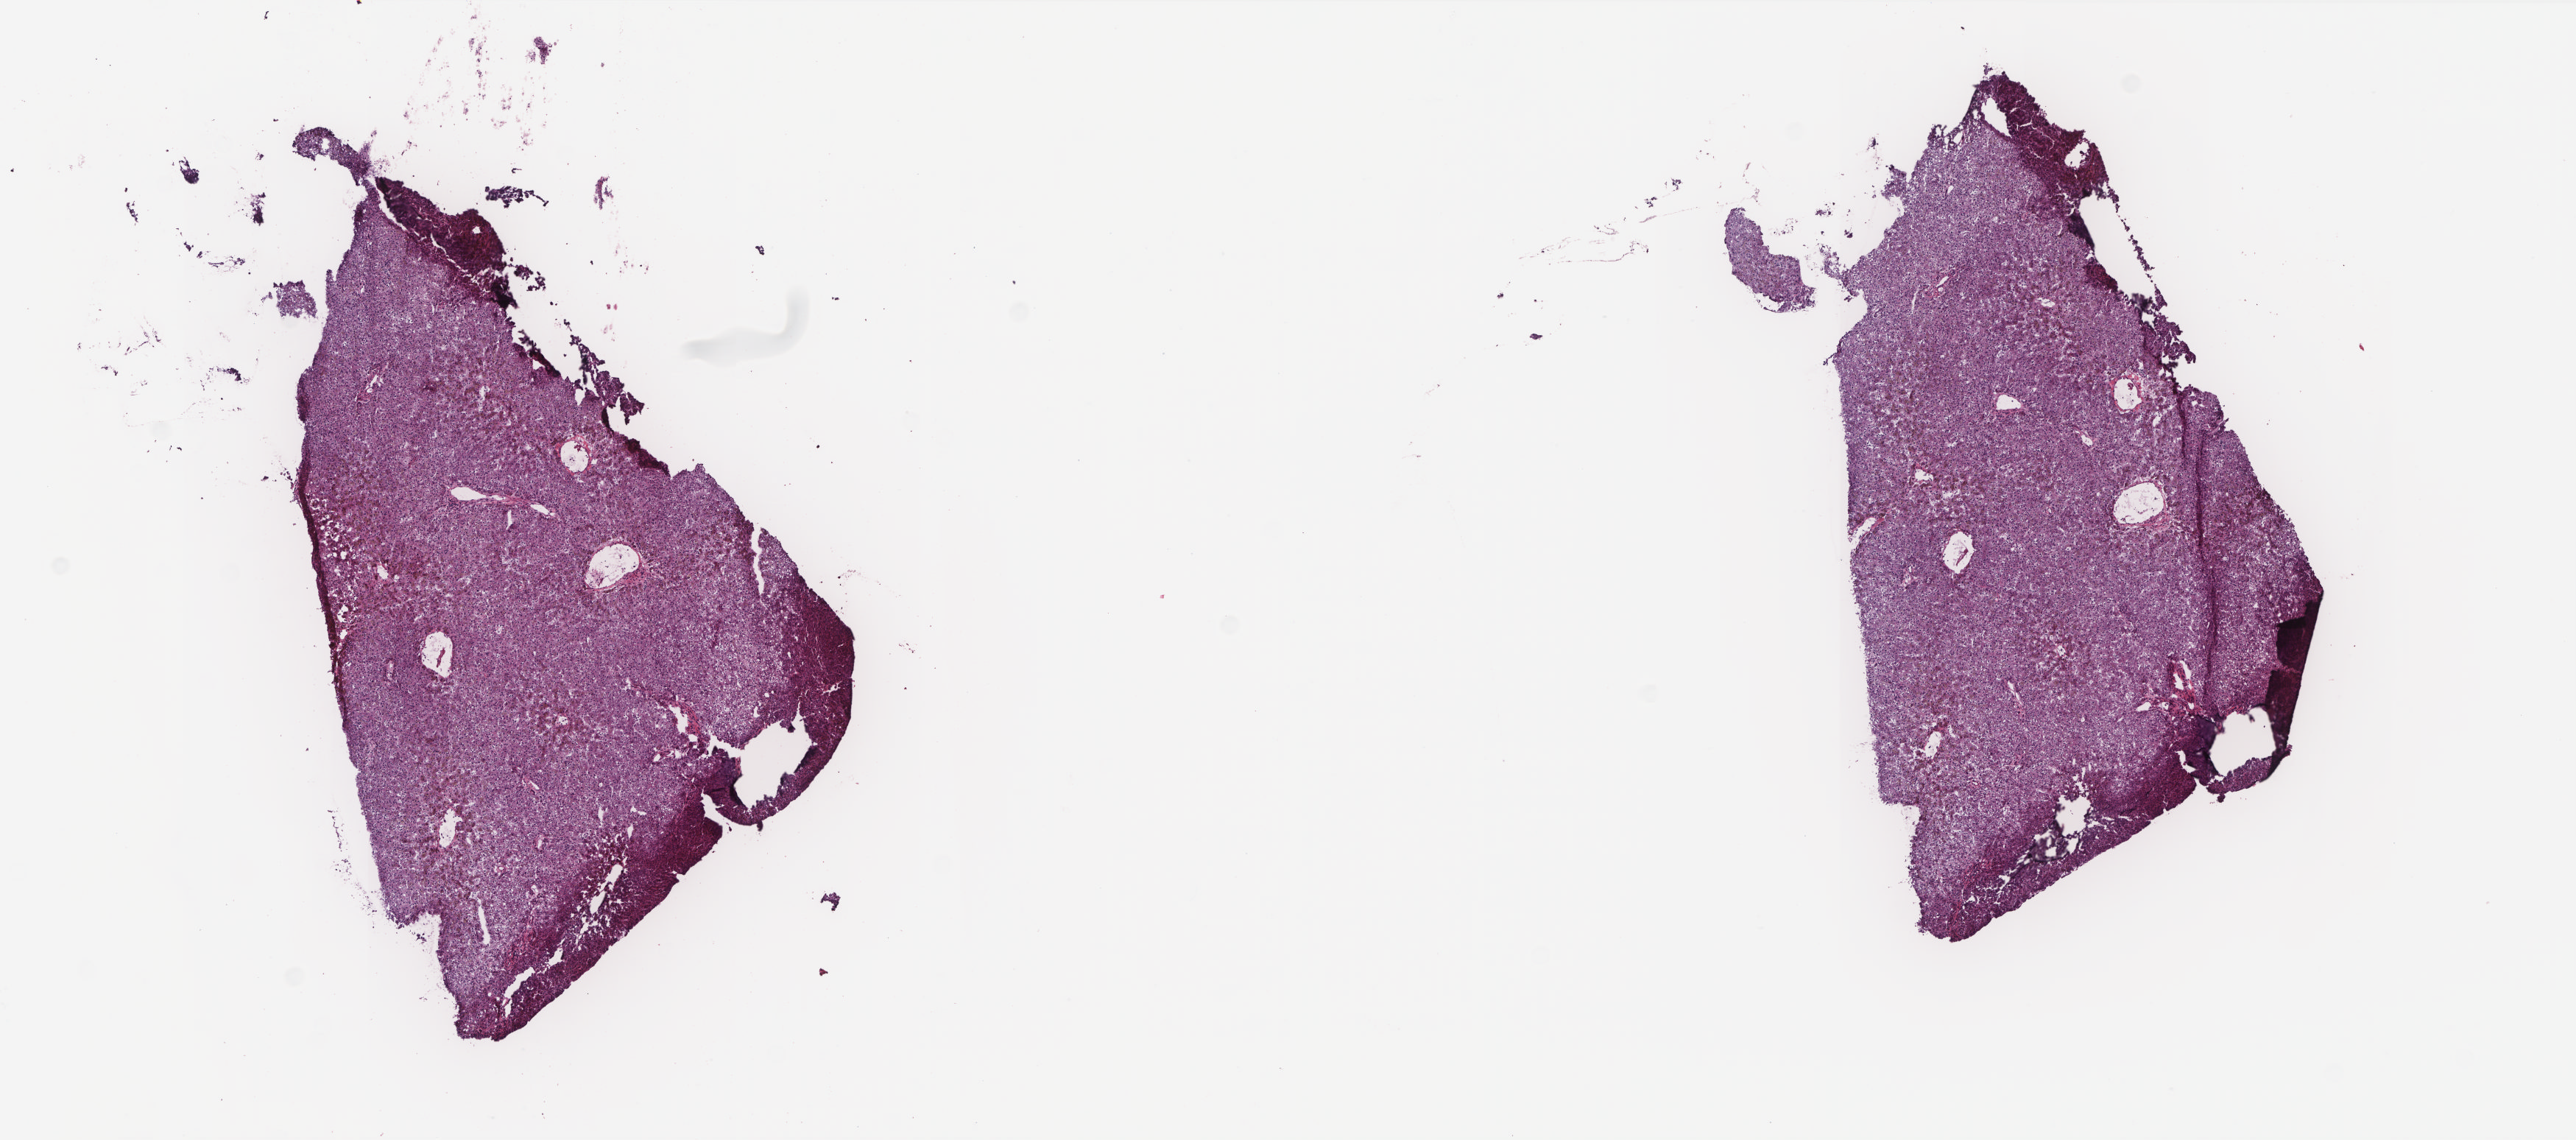
Hematoxylin and eosin (H&E) stained whole-slide image — shown as a low-resolution overview of the whole scanned area (about 14.0 x 6.2 mm); frozen section; solid tissue normal (non-tumour tissue) sample from the liver. Patient: male, age at initial diagnosis 37 years. Composition of this section per pathologist review: tumour cells 0%, tumour nuclei 0%, normal cells 100%, stromal cells 0%, necrosis 0%. Inflammatory infiltration, as recorded: lymphocyte infiltration 0%, monocyte infiltration 0%, neutrophil infiltration 0%.
- this section: solid tissue normal (non-tumour) sample from the same patient
- patient diagnosis: Hepatocellular carcinoma, NOS